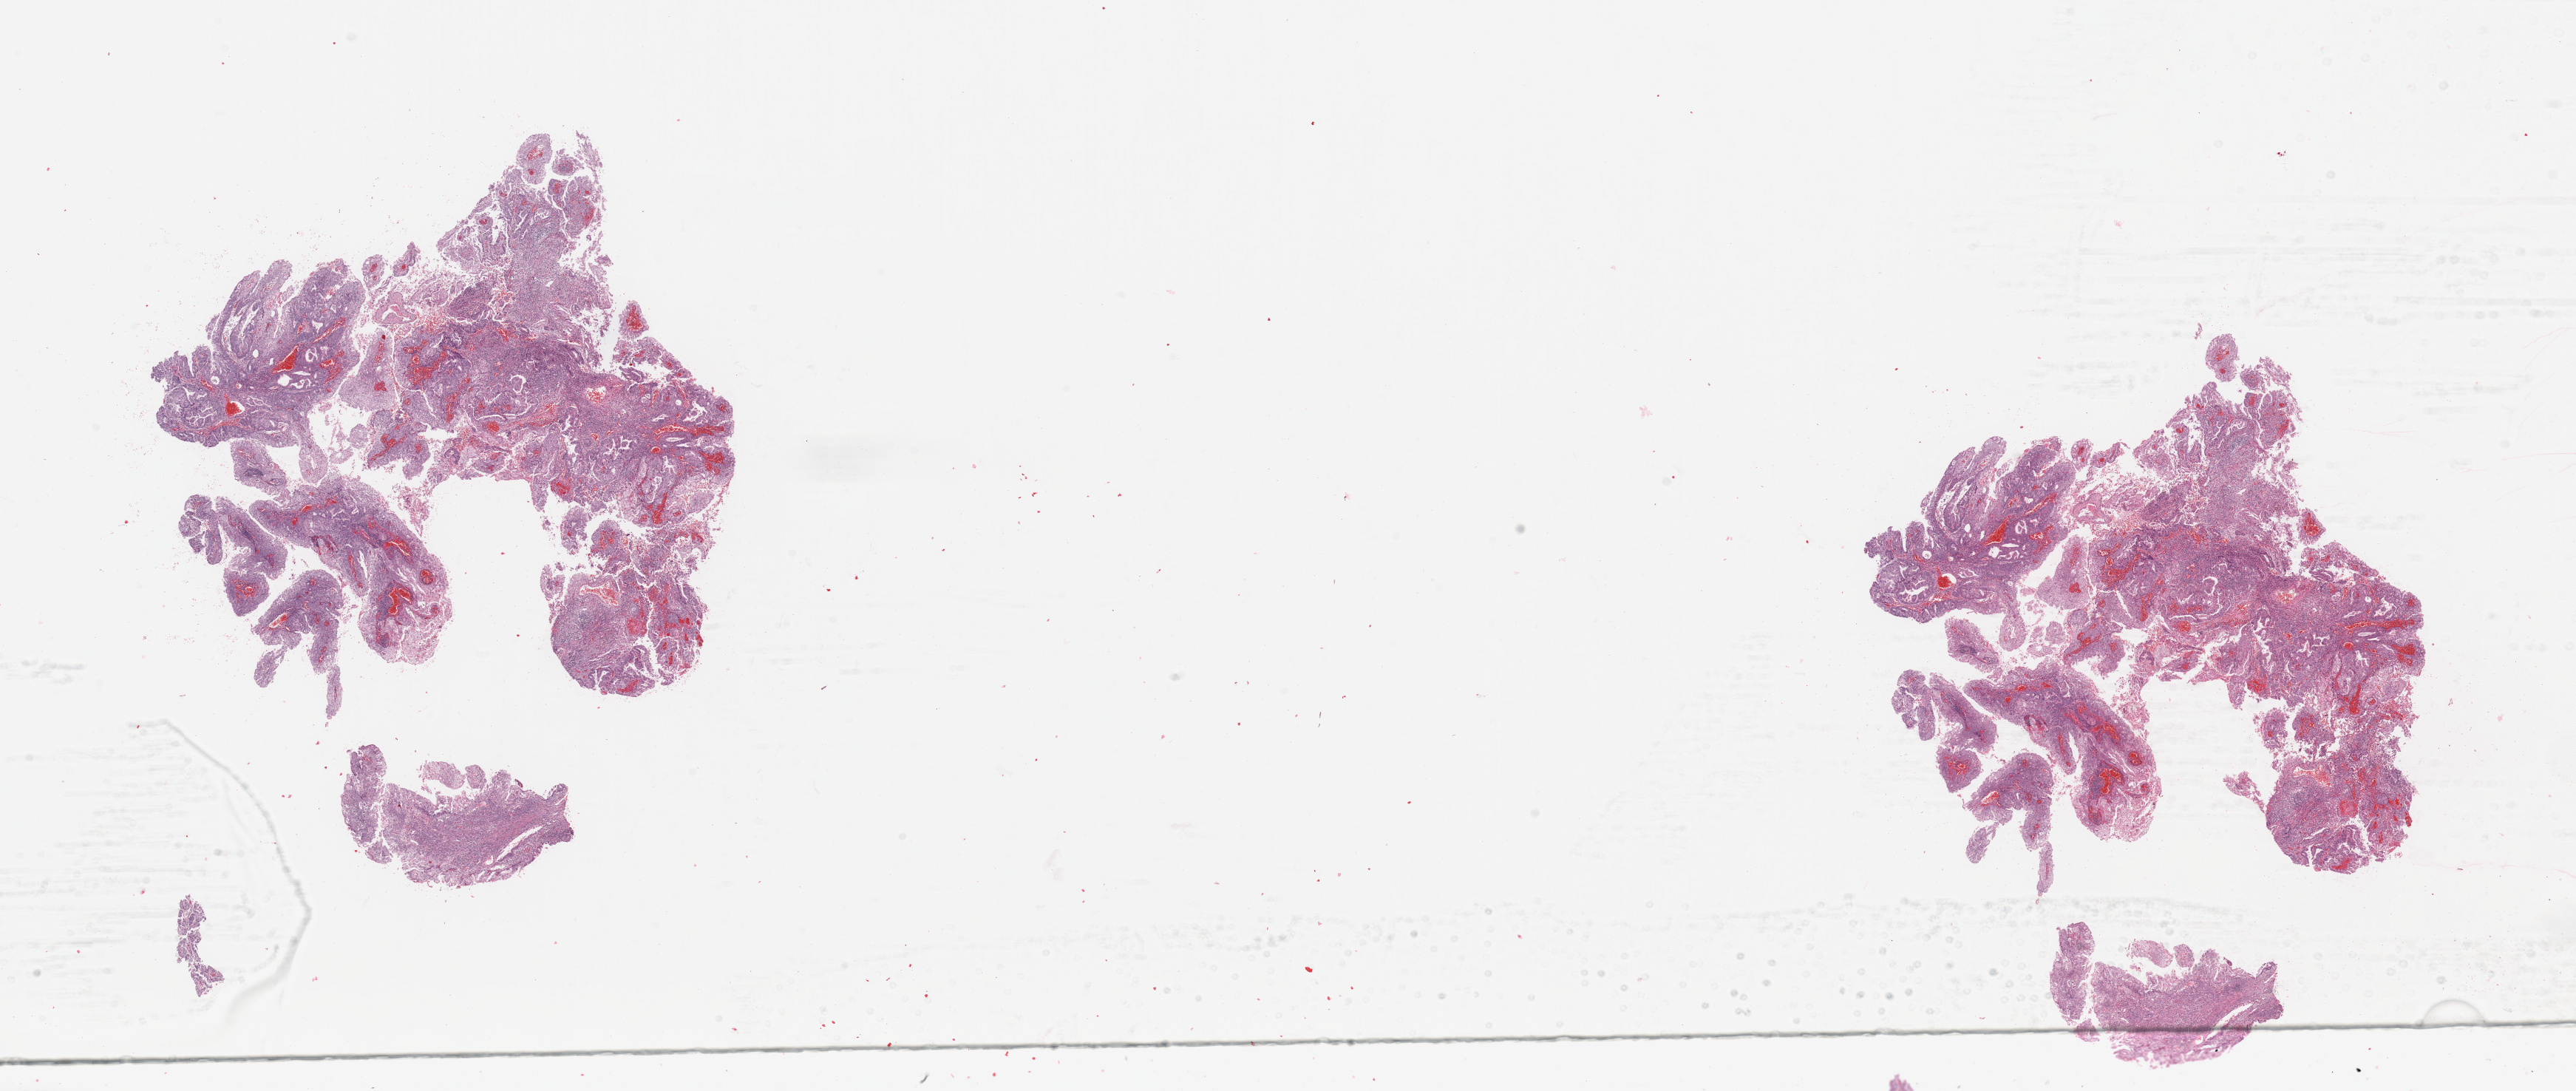
Whole-slide histology image, Hematoxylin and eosin (H&E) stained — a low-resolution overview of the entire scanned area, about 27.6 x 11.7 mm, tumour tissue sample, uterus. 74-year-old female patient. Histologic grade: G2 (moderately differentiated).
Histologic diagnosis: Endometrioid adenocarcinoma, NOS. AJCC pathologic stage: IIIC1.